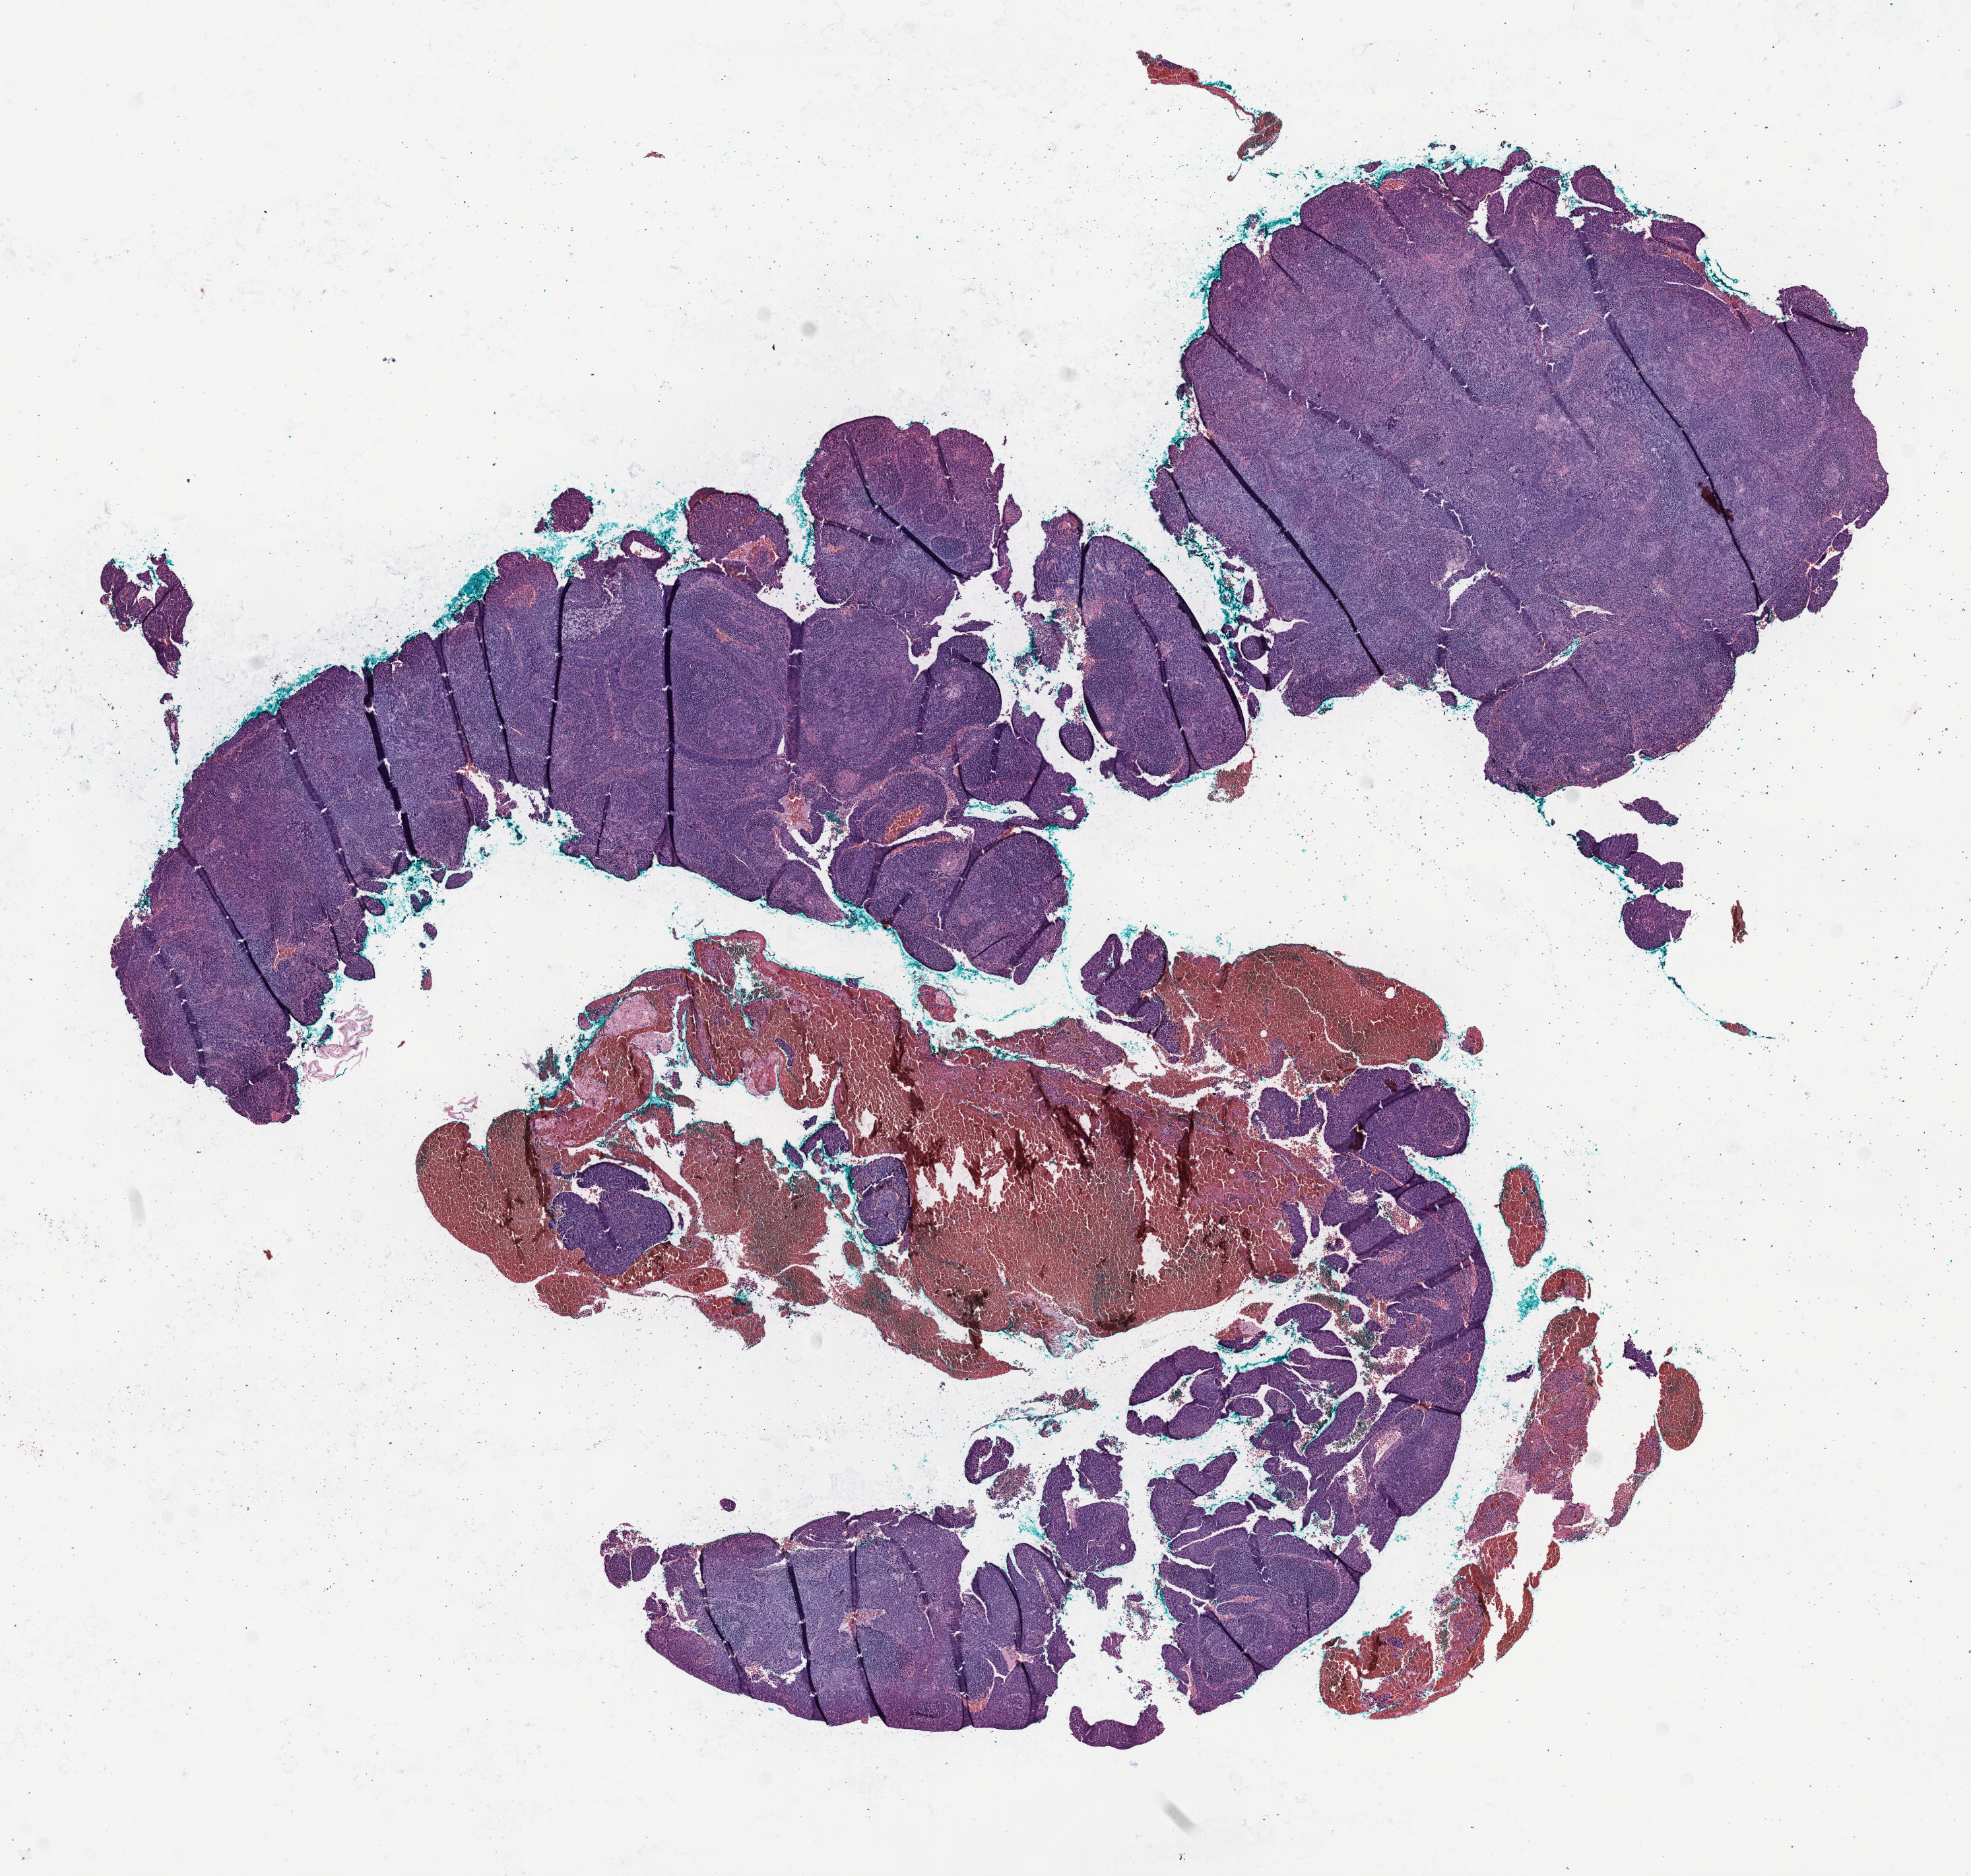
H&E-stained whole-slide image, shown as a low-resolution overview of the whole scanned area (about 12.1 x 11.5 mm); formalin-fixed paraffin-embedded (FFPE) diagnostic section; sample: primary tumour, cervix. Patient: female, age at initial diagnosis 57 years. Histologic grade: G3 (poorly differentiated).
Diagnosis: Squamous cell carcinoma, NOS (cervix uteri). FIGO stage: IIB.